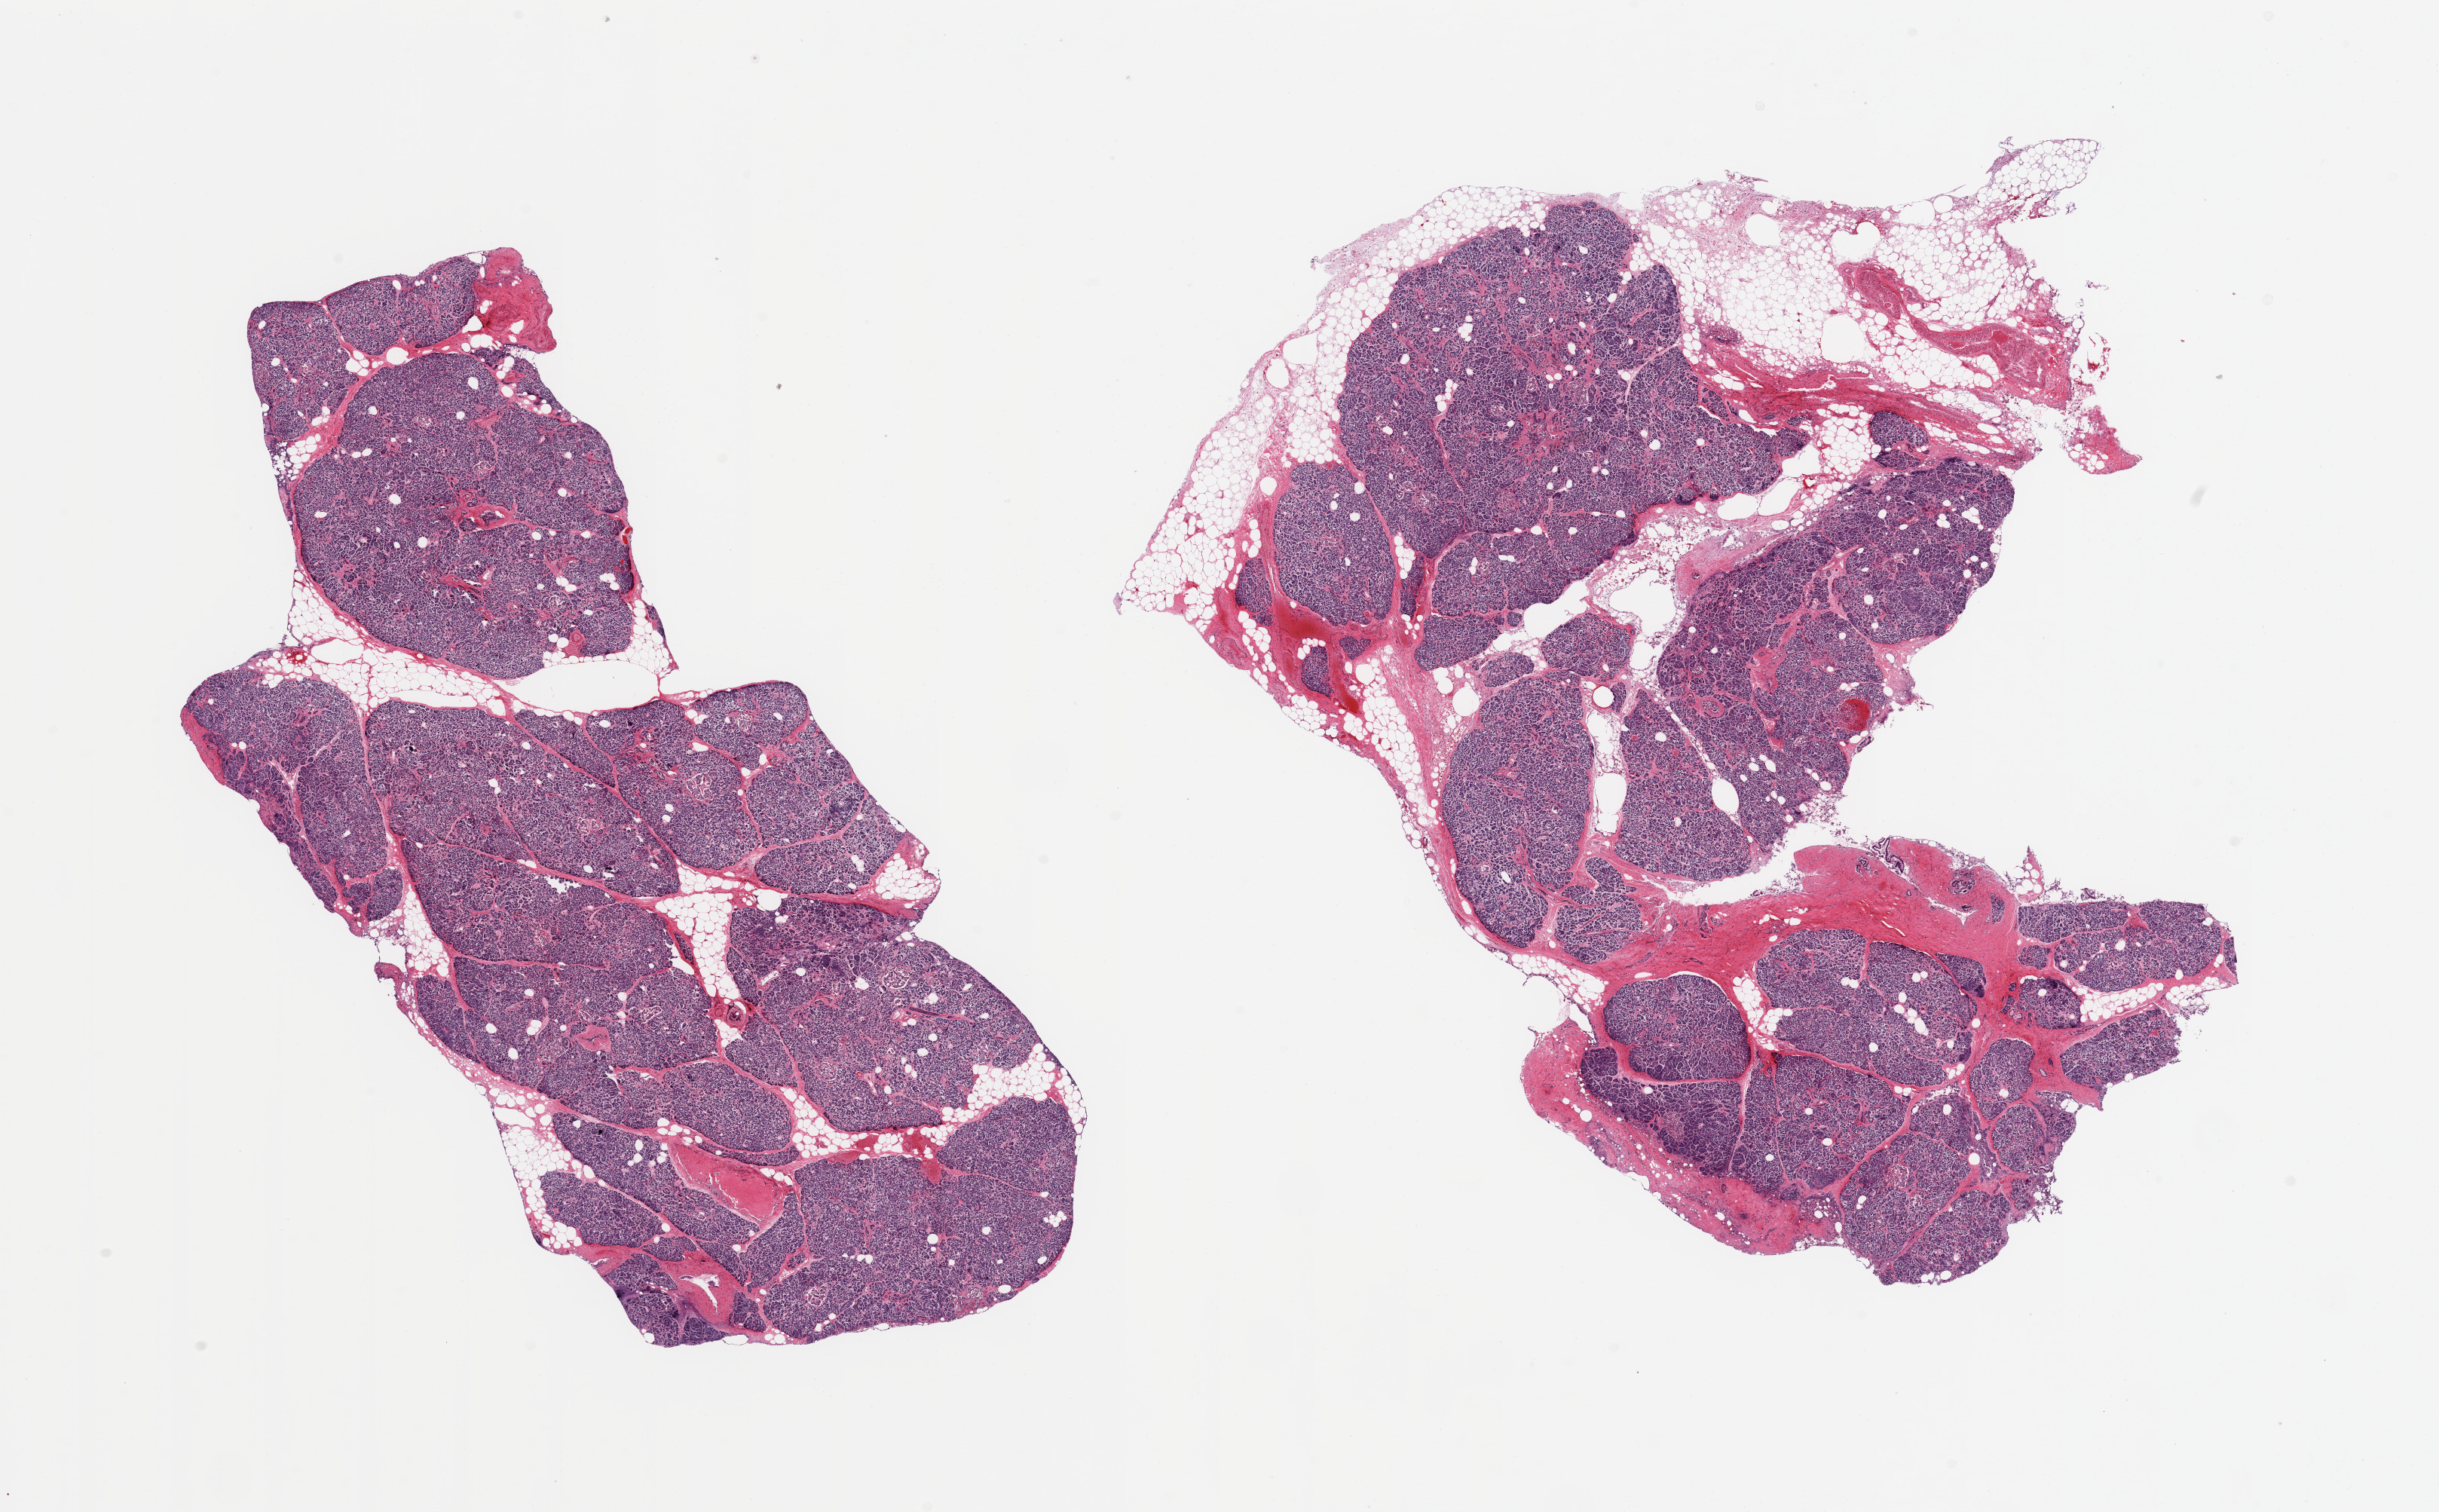
Haematoxylin and eosin whole-slide image, whole scanned area (about 25.6 x 15.9 mm) shown as a low-resolution overview, PAXgene-fixed paraffin-embedded (PFPE) section, section of pancreas (target tissue), tissue donor sample. Female donor.
Review note (as recorded): 2 pieces; include 5-15% fat, mild fibrosis.